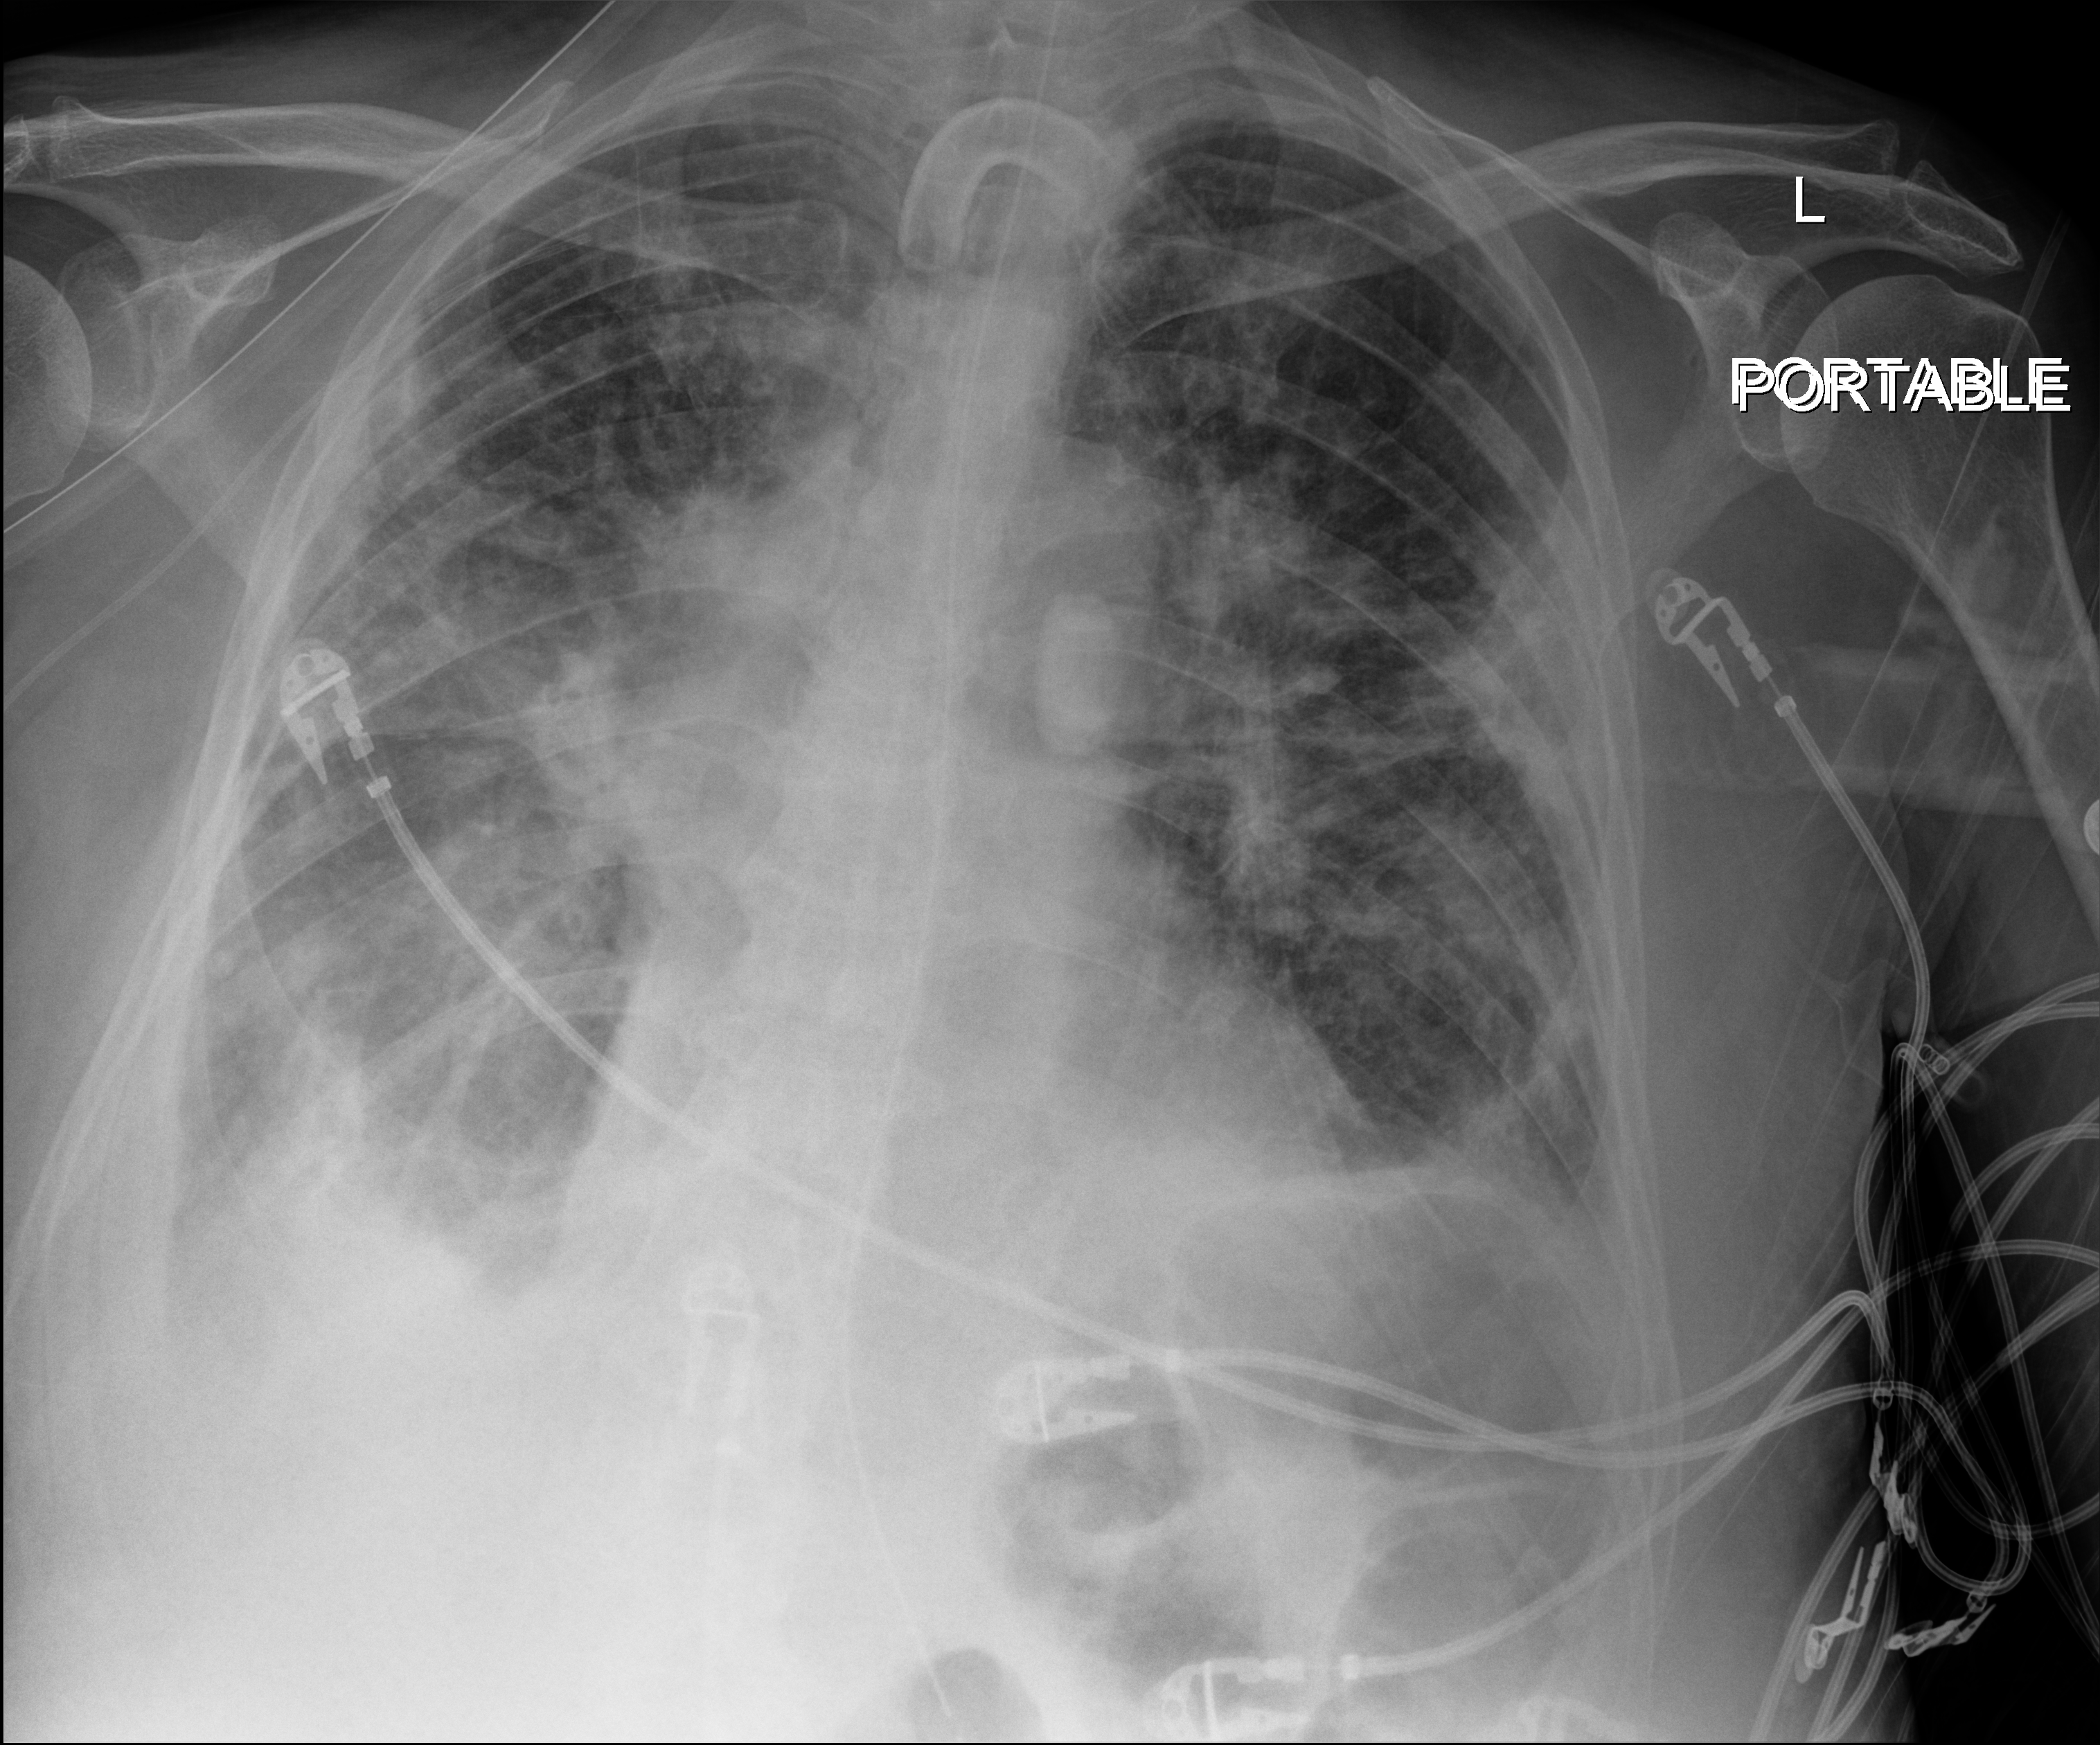
Chest X-ray (portable); anteroposterior (AP) projection. Male patient hospitalised with COVID-19, age 75–90 years.
From the hospital-stay record, not from the radiograph (when in the stay this image was taken is not recorded): length of hospital stay: 70 days; admitted to intensive care during this hospital stay: yes; mechanically ventilated during this hospital stay: yes.